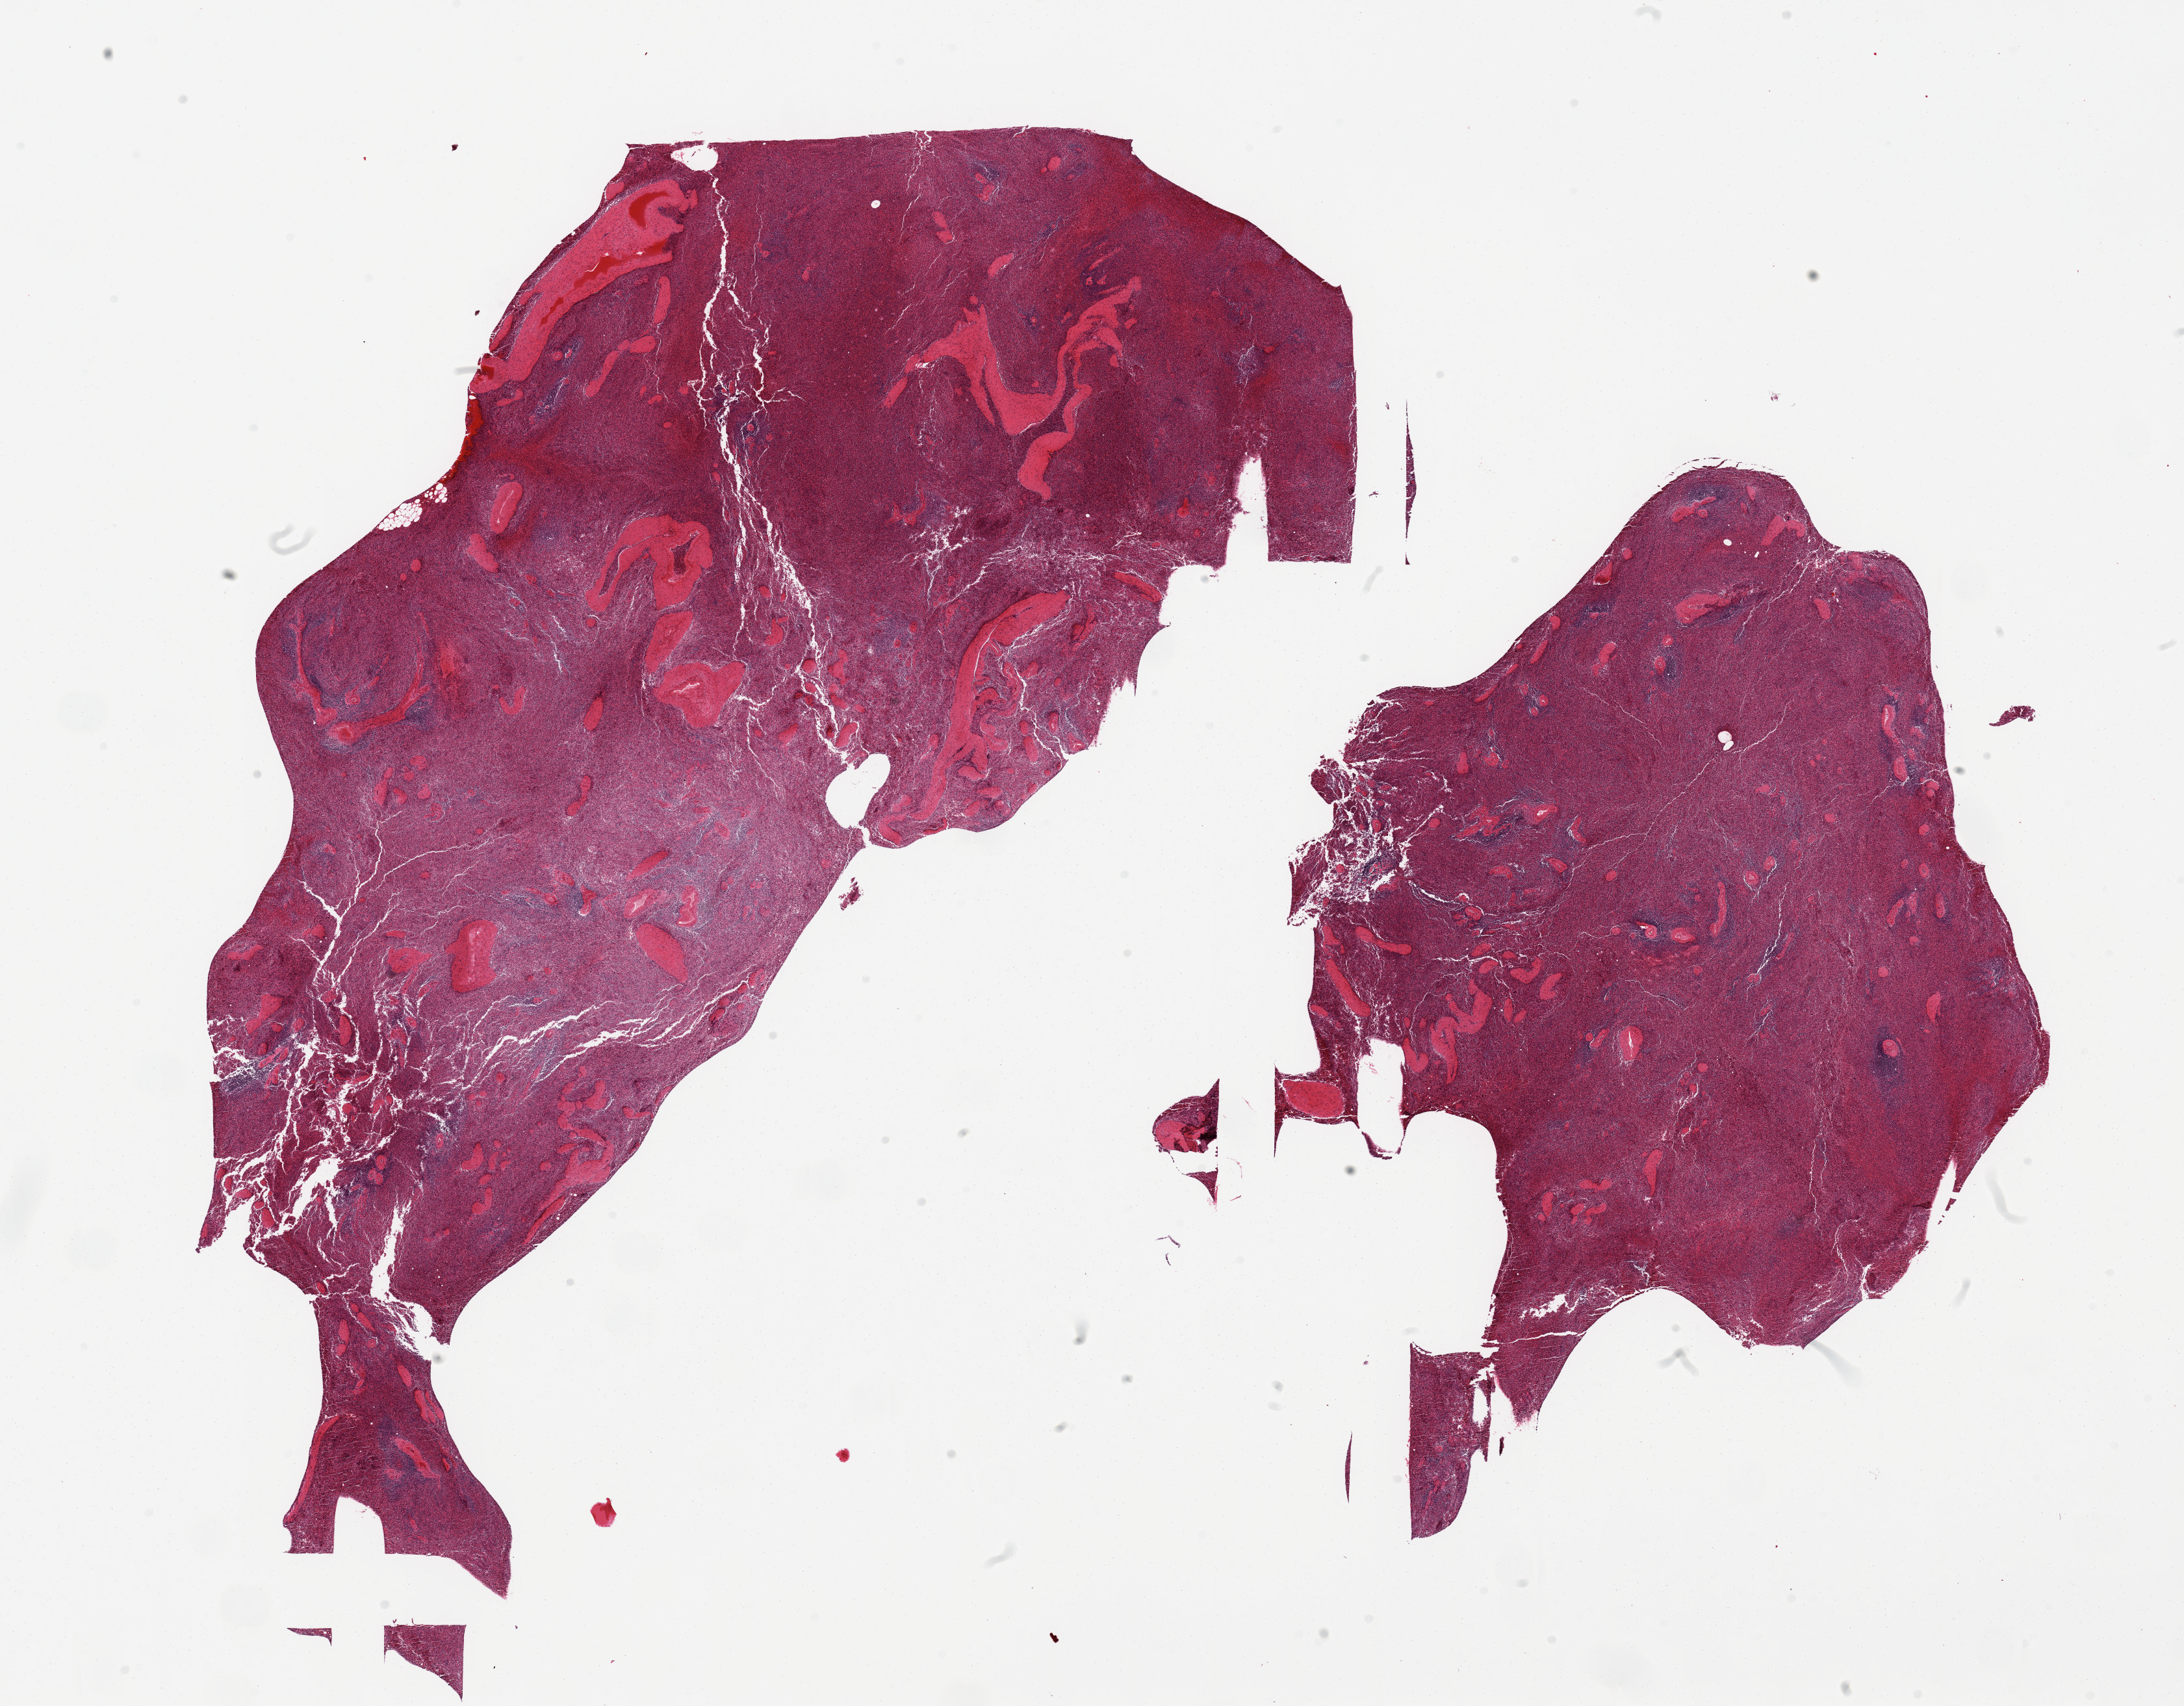
Digitized H&E-stained section — shown as a low-resolution overview of the whole scanned area (about 26.6 x 20.8 mm, acquisition: 20x scan). PAXgene-fixed, paraffin-embedded tissue. Section of spleen (target tissue). Donor tissue sample.
• pathologist's review note for this sample: 2 pieces, minimal congestion